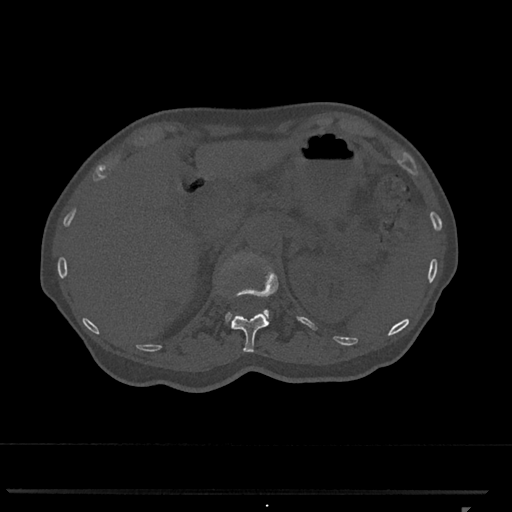
CT including the spine, one axial slice; slice 443 of 793 in the series (ordered by position); reconstruction kernel Br40s/3; 120 kVp; bone window (W 1800 / L 400 HU); 0.5 mm slice thickness; 512 × 512 image matrix, field of view 380 × 380 mm. Patient: female, 62 years. Case-level facts recorded for this patient, not image findings: primary cancer: renal.
Annotated regions visible in this slice (semi-automatic segmentation, software-assisted and operator-edited):
- L1 vertebra: bounding box [x1, y1, x2, y2] px = [225, 255, 270, 323]
- T12 vertebra: [227, 255, 278, 352]